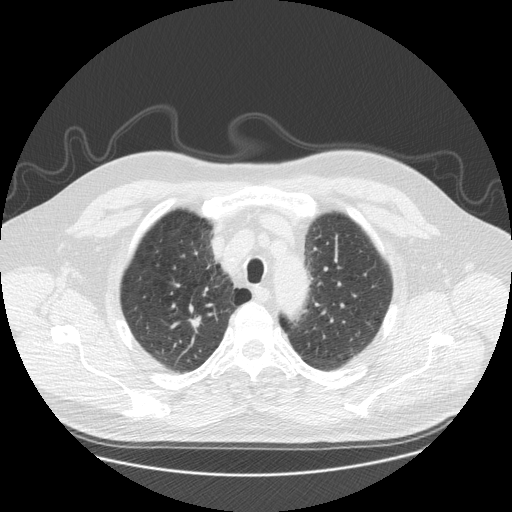
Low-dose screening chest CT, axial slice; third screening round (two years after baseline); lung window (W 1500 / L -600 HU); 2.5 mm slice thickness; standard (soft-tissue) reconstruction kernel (STANDARD); slice 31 of 173 in the series. Male participant, aged 61 years at enrolment. Former smoker at enrolment.
• Lesion marked by an expert reader, bounding box <172,303,214,336> (left, top, right, bottom; pixels).
• The exam's reader record, not a measurement of the box and not confirmed to be the same lesion: non-calcified nodule or mass ≥4 mm, right upper lobe, 10 × 7 mm, smooth margins, soft tissue attenuation, pre-existing on the prior screen: yes; interval growth: yes.
• Official screen result: positive, other.
• Later outcome: lung cancer diagnosed 110 days after this screen — squamous cell carcinoma, NOS, right upper lobe, moderately differentiated (G2), stage IA (AJCC 6th edition), 10 mm at pathology.